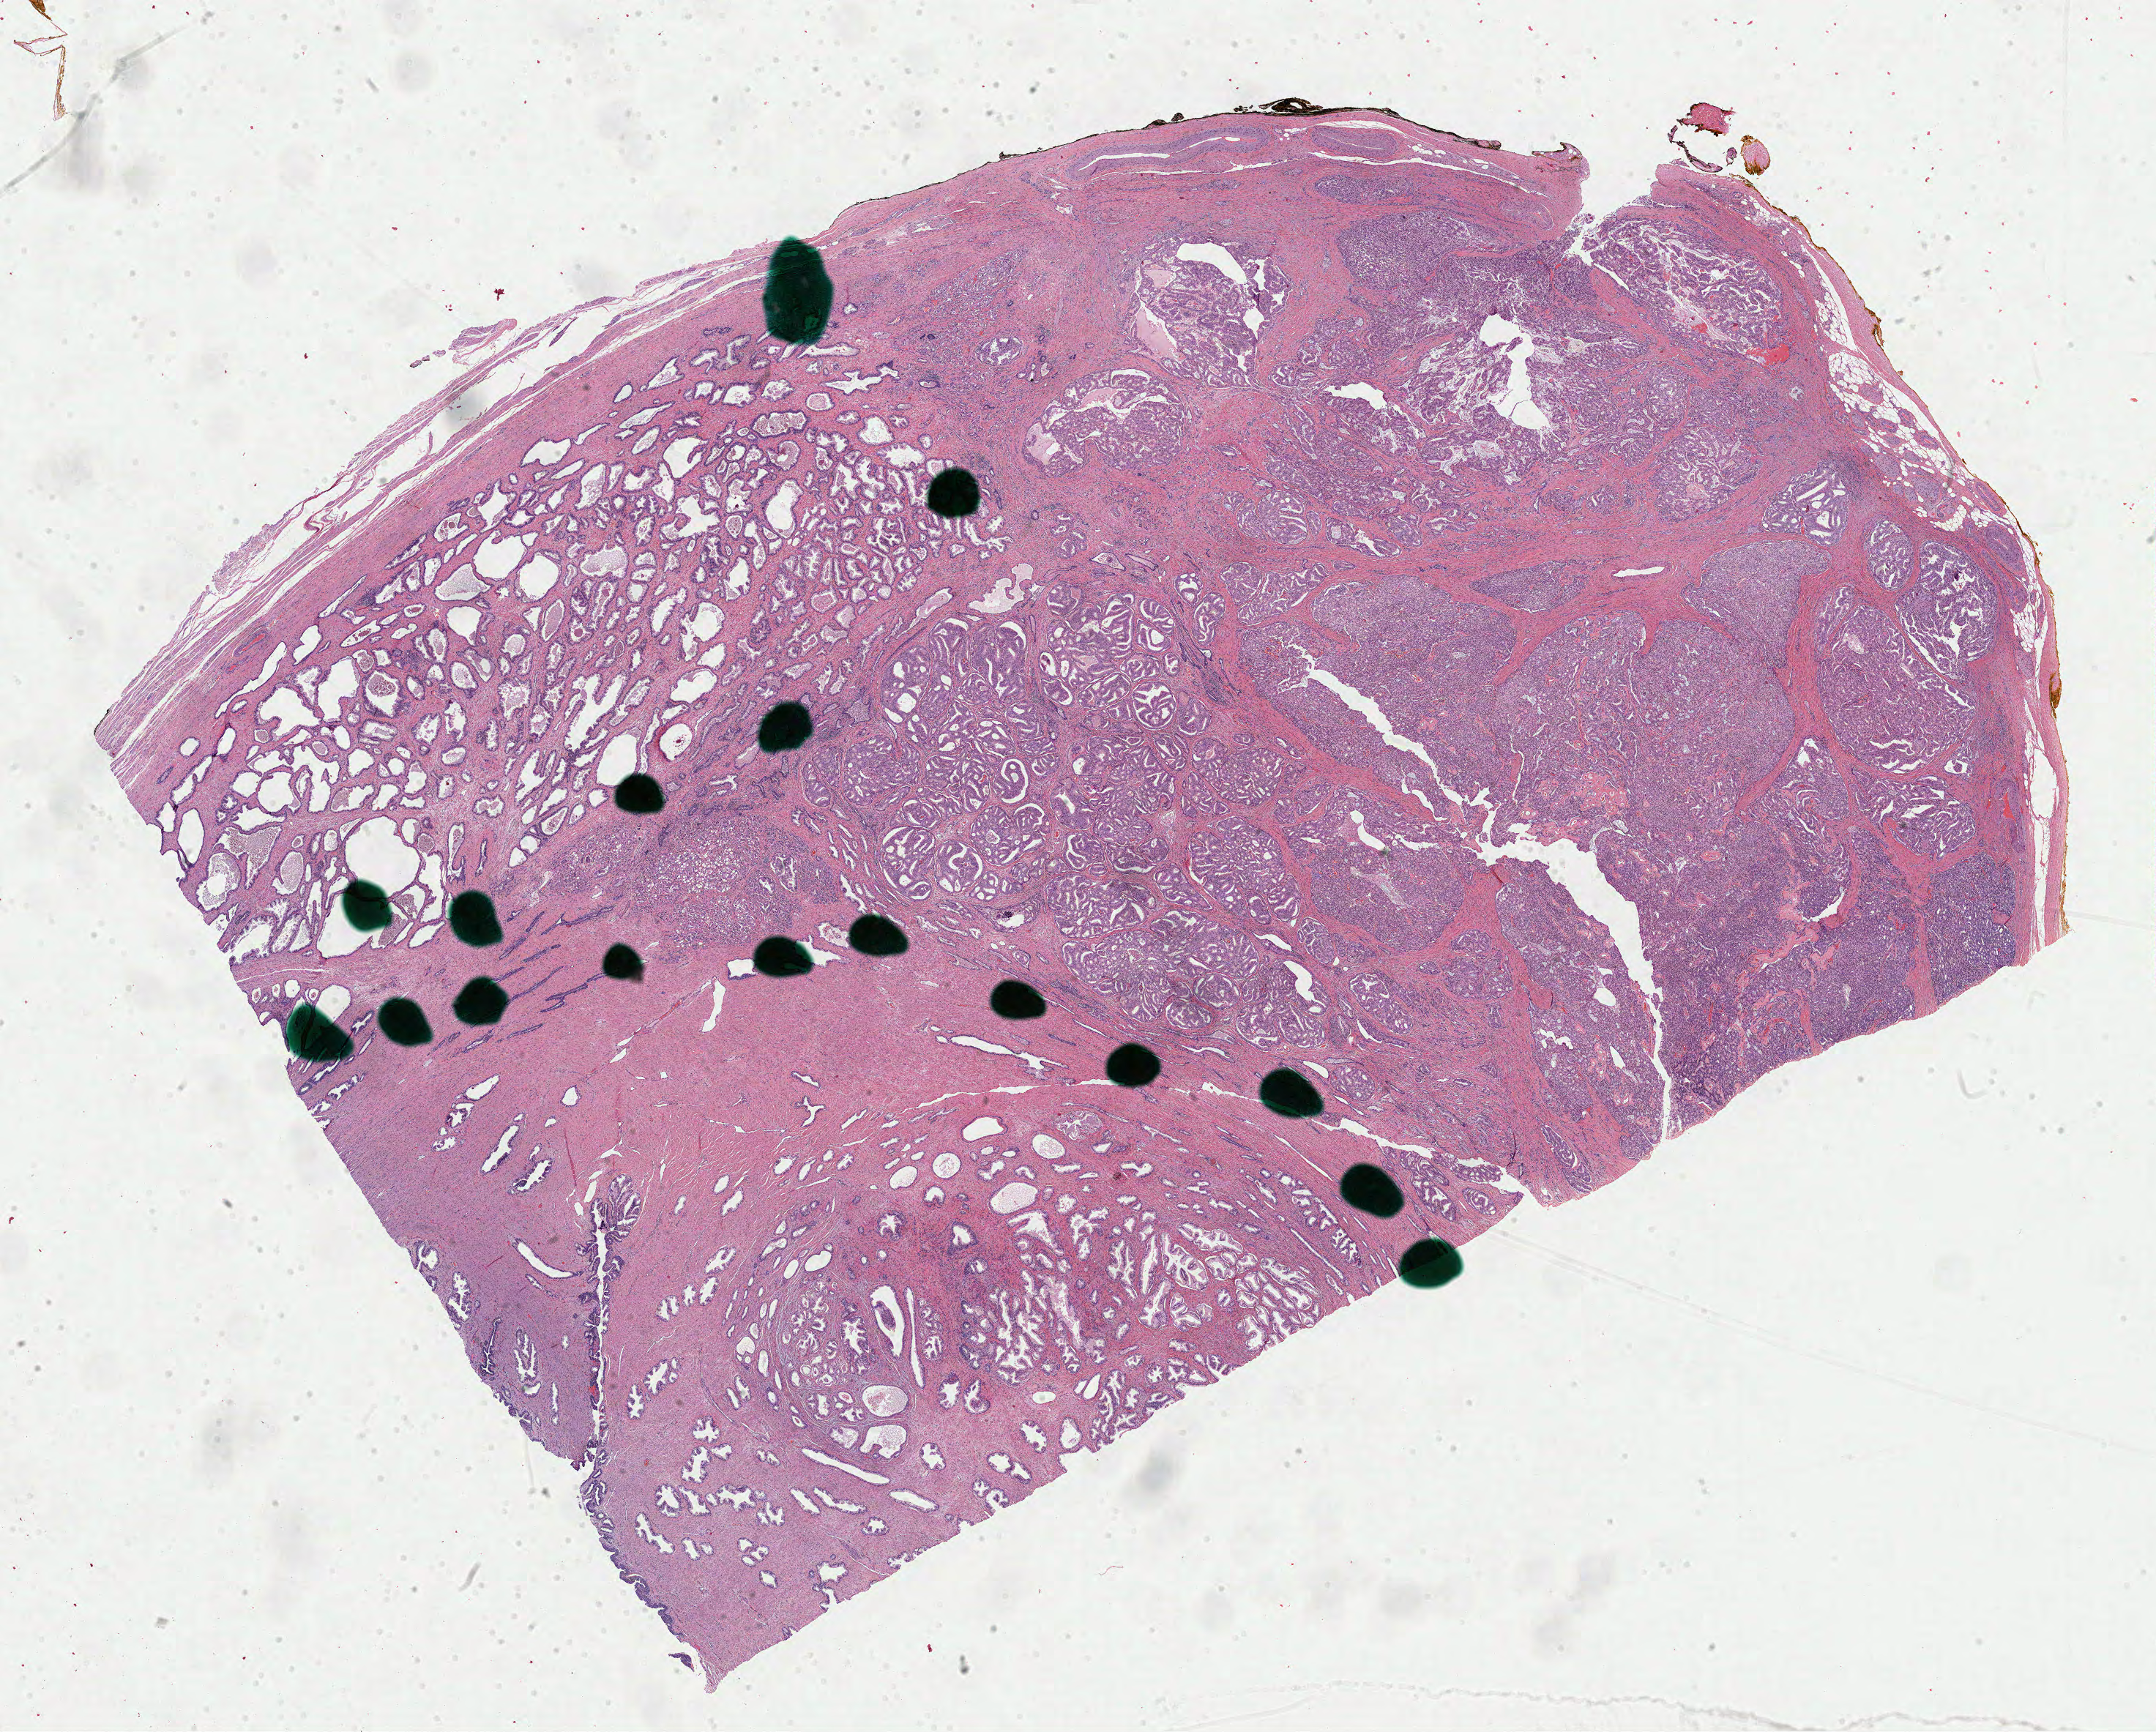
H&E-stained whole-slide image, shown as a low-resolution overview of the whole scanned area (about 23.3 x 18.7 mm, from a 40x scan). Formalin-fixed paraffin-embedded (FFPE) diagnostic section. Prostate, primary tumour sample. Male, age 59 years at initial diagnosis. Gleason score: 9 (4+5).
* histologic diagnosis: Adenocarcinoma, NOS
* laterality: right
* lymph nodes positive (case pathology): 0 of 9 examined